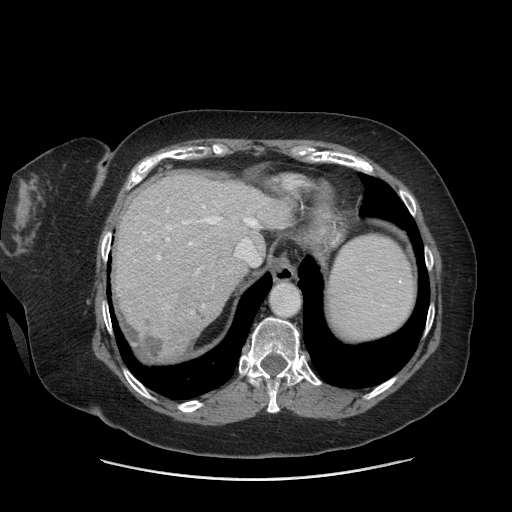
Contrast-enhanced abdominal CT (liver protocol), one axial slice; position 58 of 69 along the scan axis; soft-tissue window (W 400 / L 40 HU); 2.5 mm slice thickness; 512 × 512 image matrix, field of view 420 × 420 mm. From the clinical record (not read from this slice): diagnosis: hepatocellular carcinoma (patient treated with transarterial chemoembolisation; whether this scan precedes or follows treatment is not stated here); TNM stage (as recorded): Stage-IIIB; Child-Pugh class: A; tumour differentiation: moderately differentiated.
Outlined on this slice (semi-automatic segmentation, software-assisted and operator-edited):
- abdominal aorta: box from (x=271, y=283) to (x=300, y=316) px
- liver parenchyma outside the tumour (the mass and vessels are separate outlines, so this box may not span the whole liver): (x=114, y=172)–(x=292, y=350)
- mass: (x=141, y=310)–(x=192, y=357)
- liver vessels: (x=143, y=205)–(x=259, y=307)